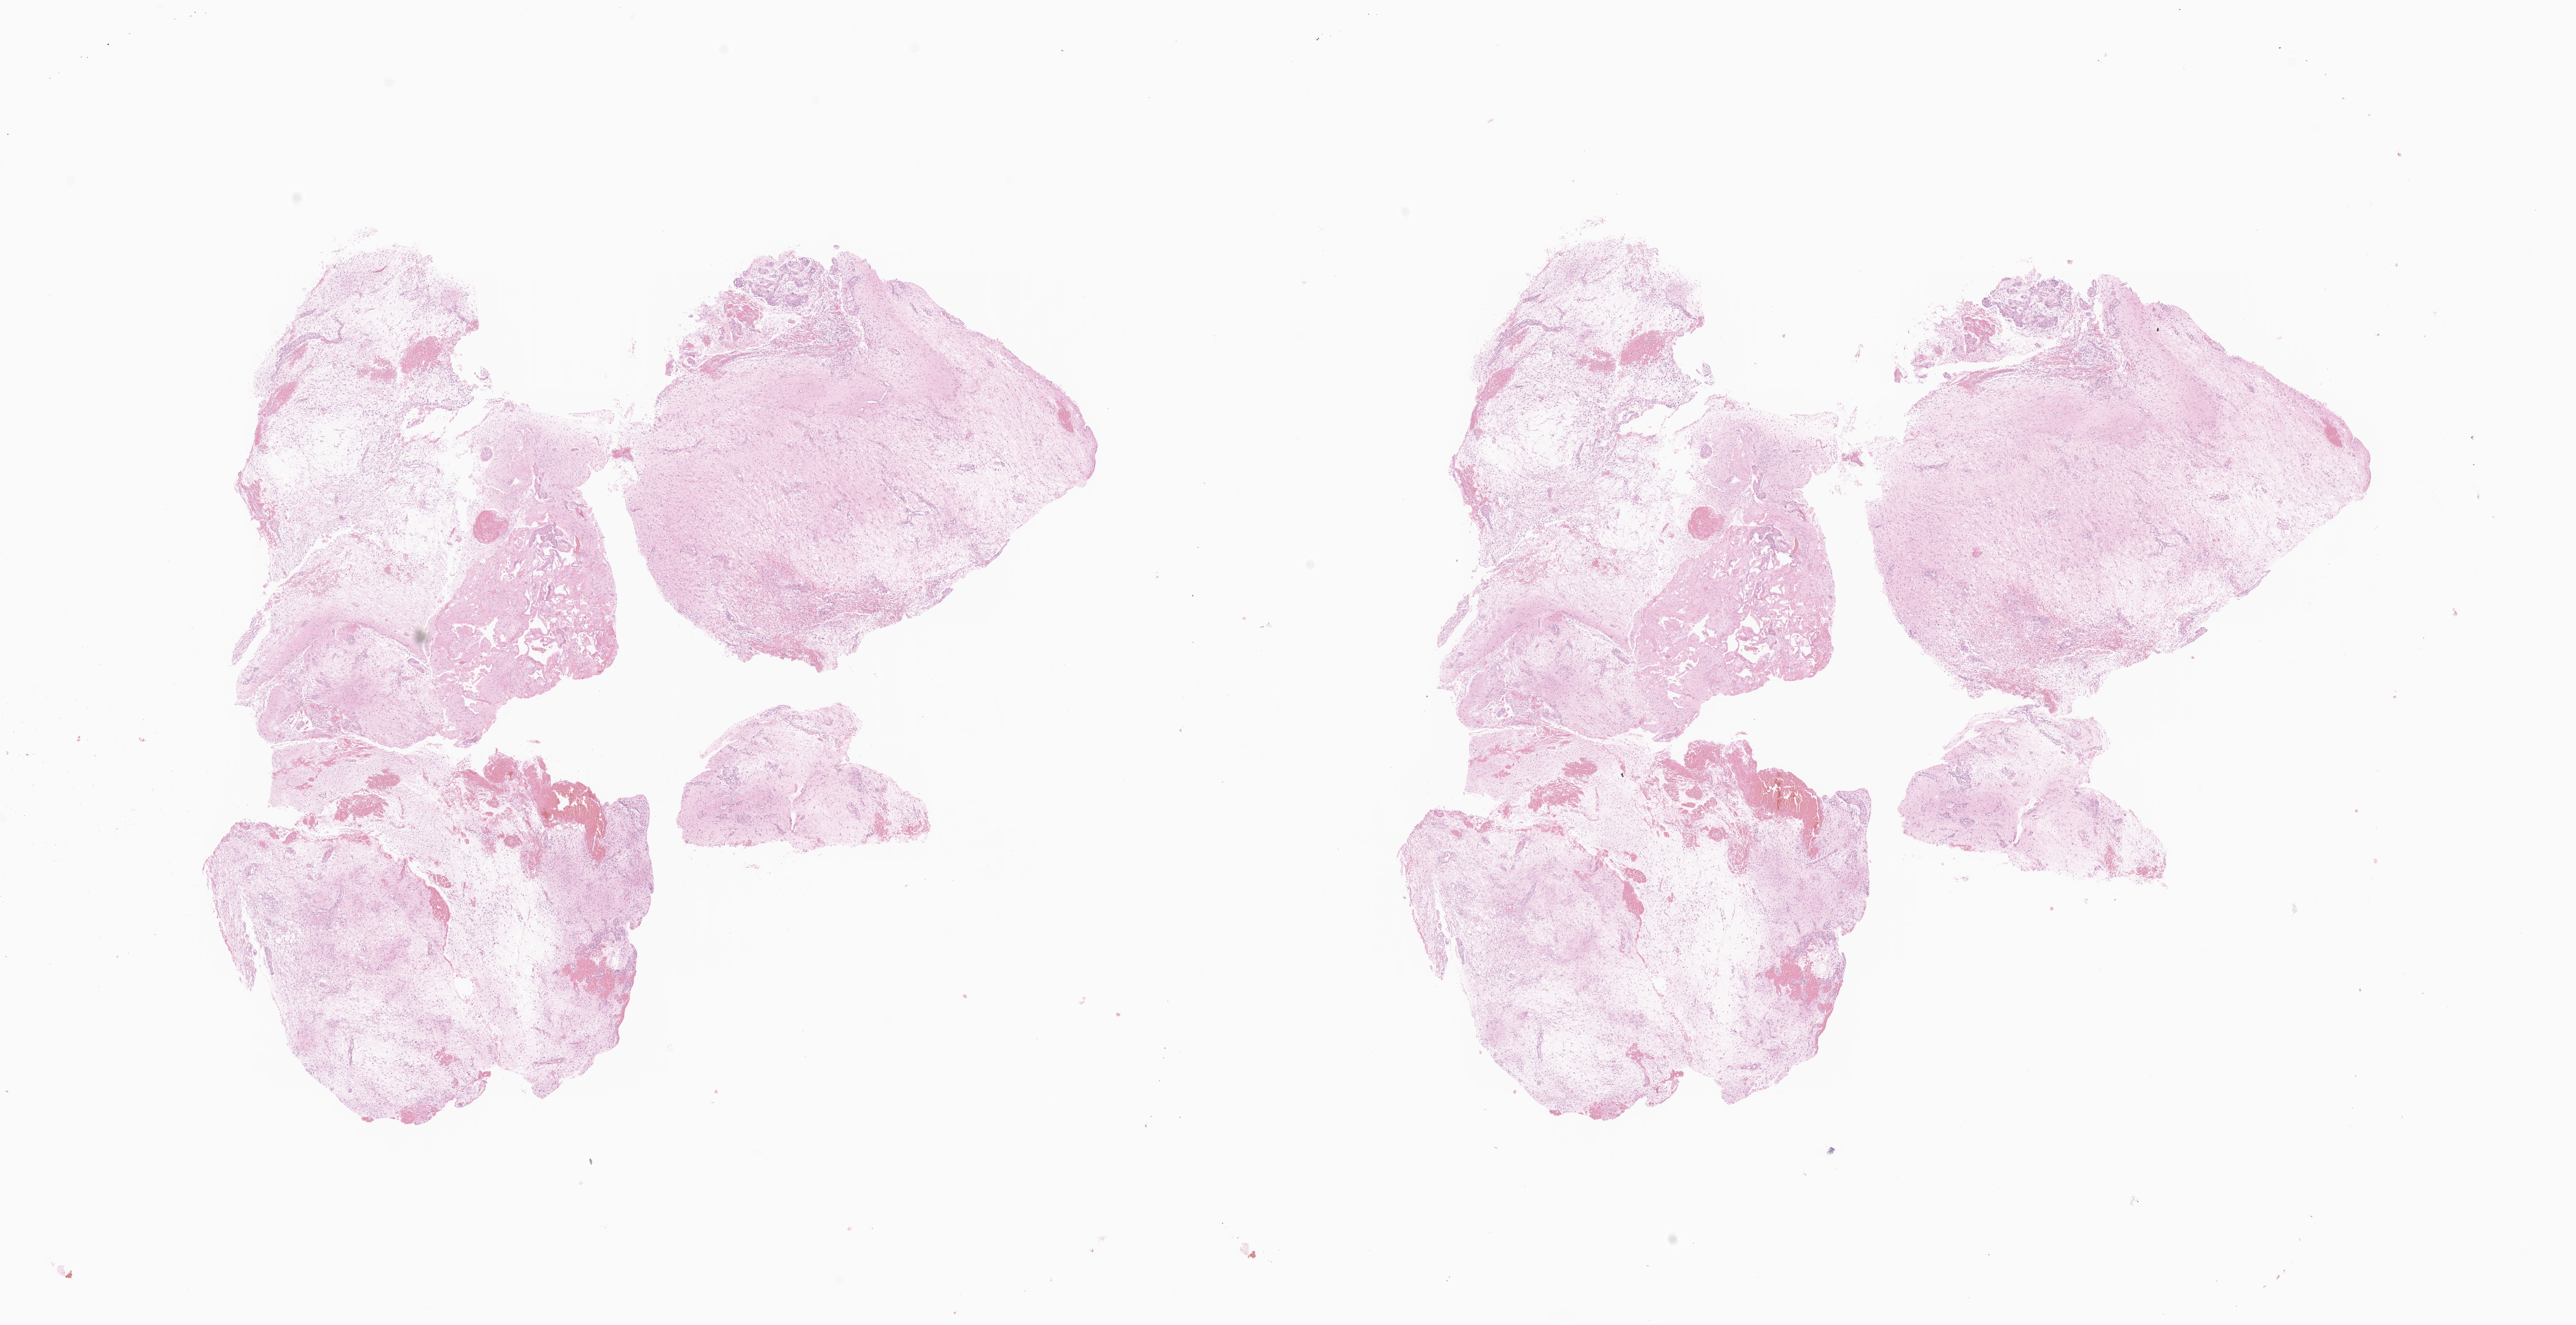
Whole-slide image, H&E stain of tumor tissue from the temporal lobe, low-resolution overview of the scanned area, about 23.4 x 12.0 mm, formalin-fixed paraffin-embedded section. Patient male; age 77 months (6 years 5 months).
Recorded diagnosis: Pilocytic astrocytoma.